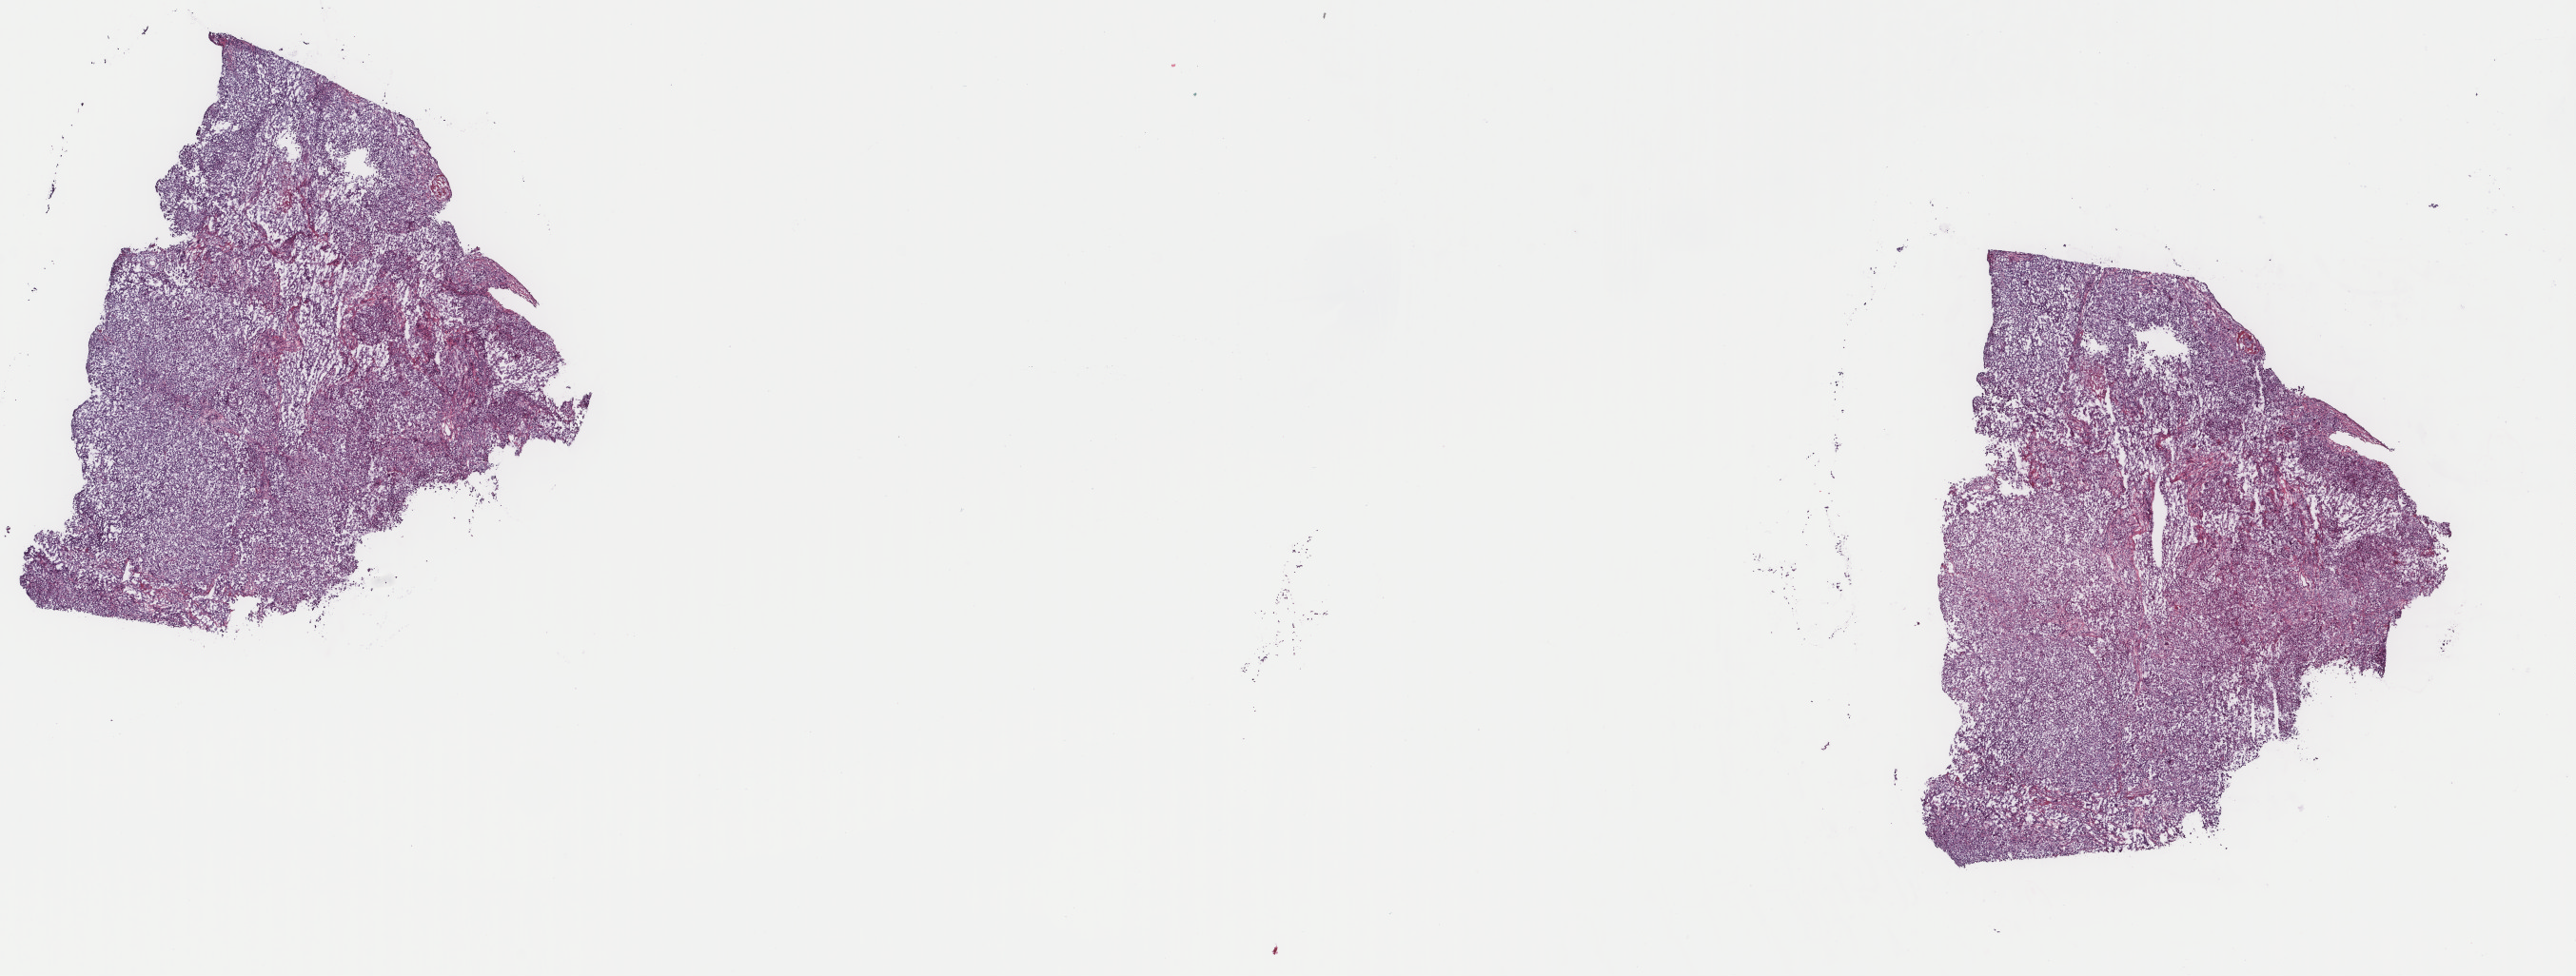
Digitized H&E tissue section (whole slide) — low-resolution overview of the scanned area, about 21.5 x 8.1 mm (from a 40x scan), frozen section, primary tumour sample from the mesothelium. Female, age 56 years at initial diagnosis. Pathologist review of this section (percent, as recorded): tumour cells 100%, tumour nuclei 95%, normal cells 0%, stromal cells 0%, necrosis 0%. Infiltration values recorded for this section: lymphocyte infiltration 0%, monocyte infiltration 0%, neutrophil infiltration 0%.
• pathologic diagnosis: Epithelioid mesothelioma, malignant
• AJCC pathologic stage: III